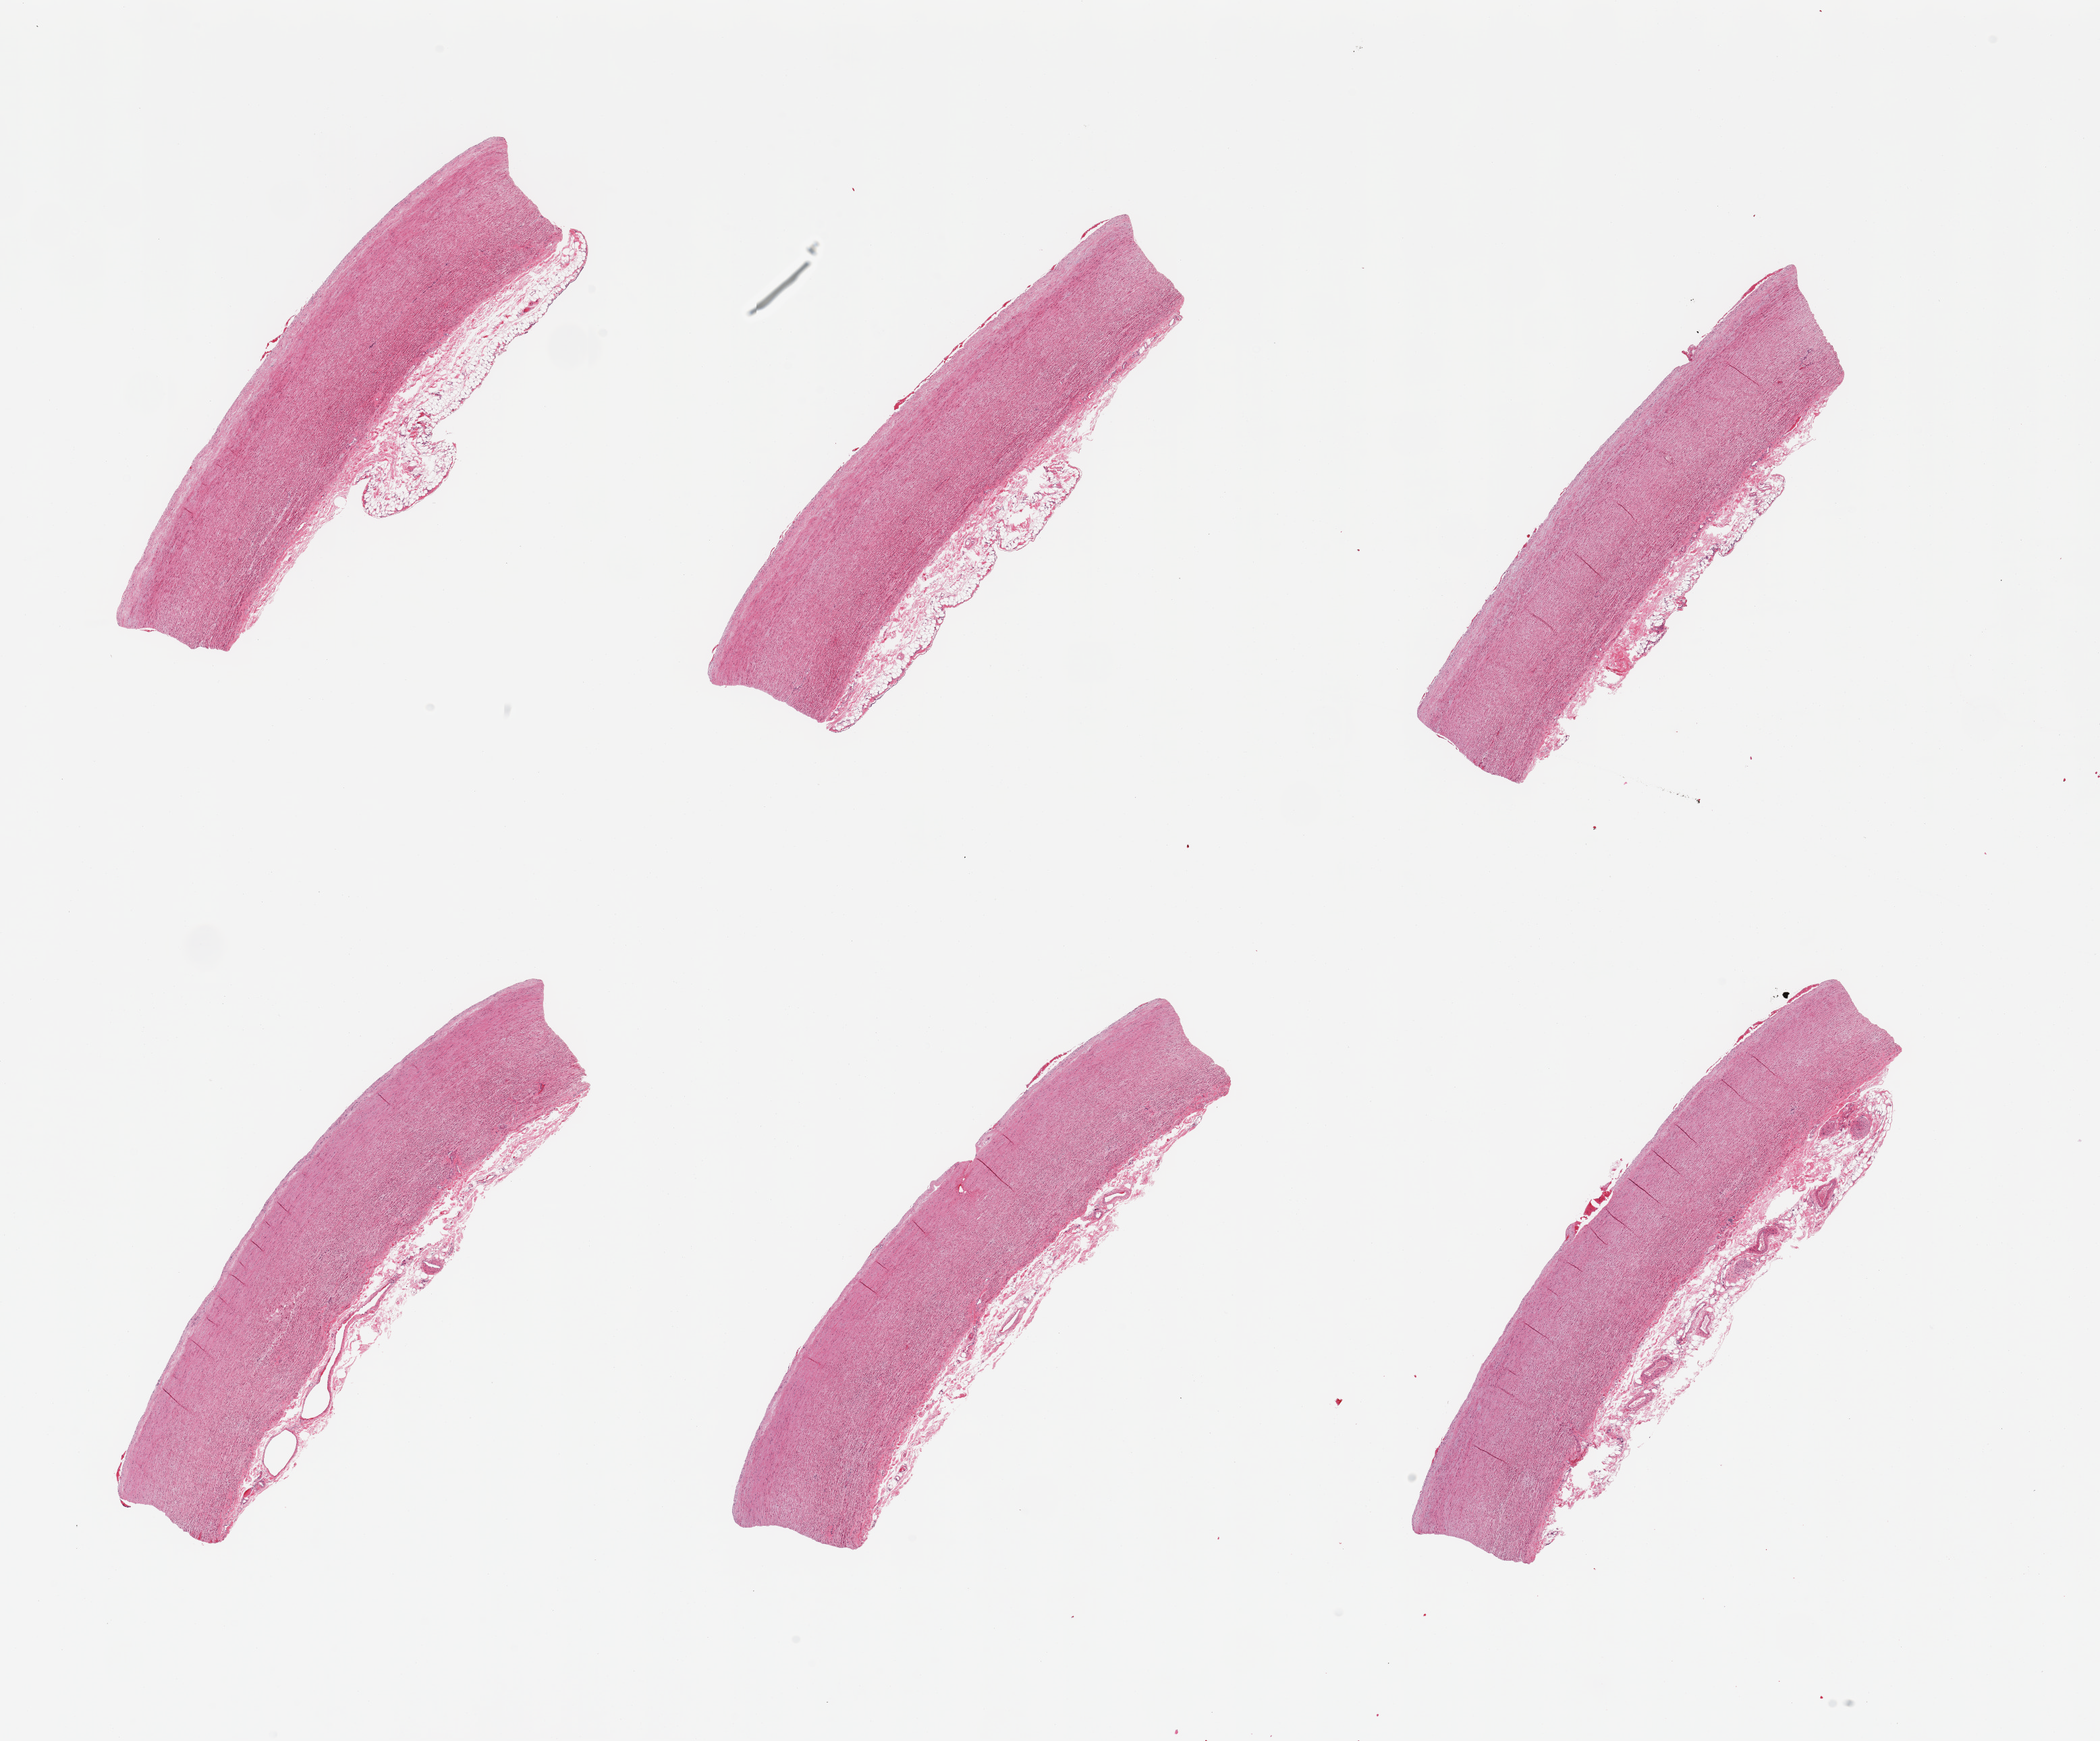
Haematoxylin and eosin whole-slide image — low-resolution overview of the scanned area, about 24.6 x 20.4 mm, PAXgene-fixed paraffin-embedded (PFPE) section, section of aorta (target tissue), donor tissue sample. Female donor.
Reviewer comment on this tissue sample: 6 pieces; thin plaques; adventitial fat up to 0.7 mm thick.